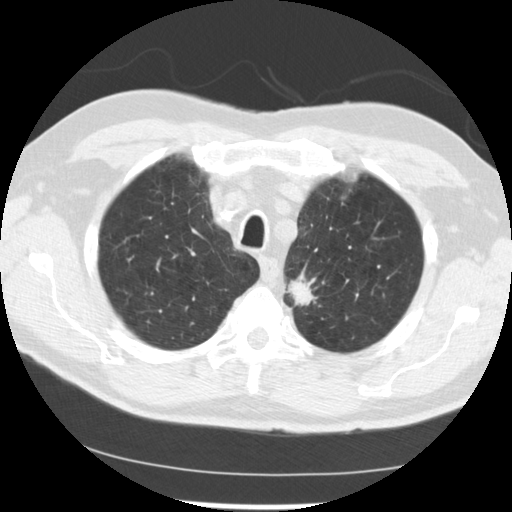
Low-dose screening chest CT, axial slice, baseline screening round, lung window (W 1500 / L -600 HU), 2.5 mm slice thickness, standard (soft-tissue) reconstruction kernel (STANDARD). Male, age 71 years at enrolment. Current smoker at enrolment.
Expert reader's lesion annotation, bounding box (x1, y1, x2, y2) in pixels: (273, 264, 334, 317). The screening reader recorded 2 non-calcified nodules or masses ≥4 mm on this exam (left upper lobe, left upper lobe); which of them this box marks is not recorded. Official screen result: positive, change unspecified: nodule(s) >= 4 mm or enlarging nodule(s), mass(es), or other non-specific abnormalities suspicious for lung cancer. Lung cancer was diagnosed 37 days after this screen: adenocarcinoma, NOS, left upper lobe, poorly differentiated (G3), stage IIIB (AJCC 6th edition), 25 mm at pathology.